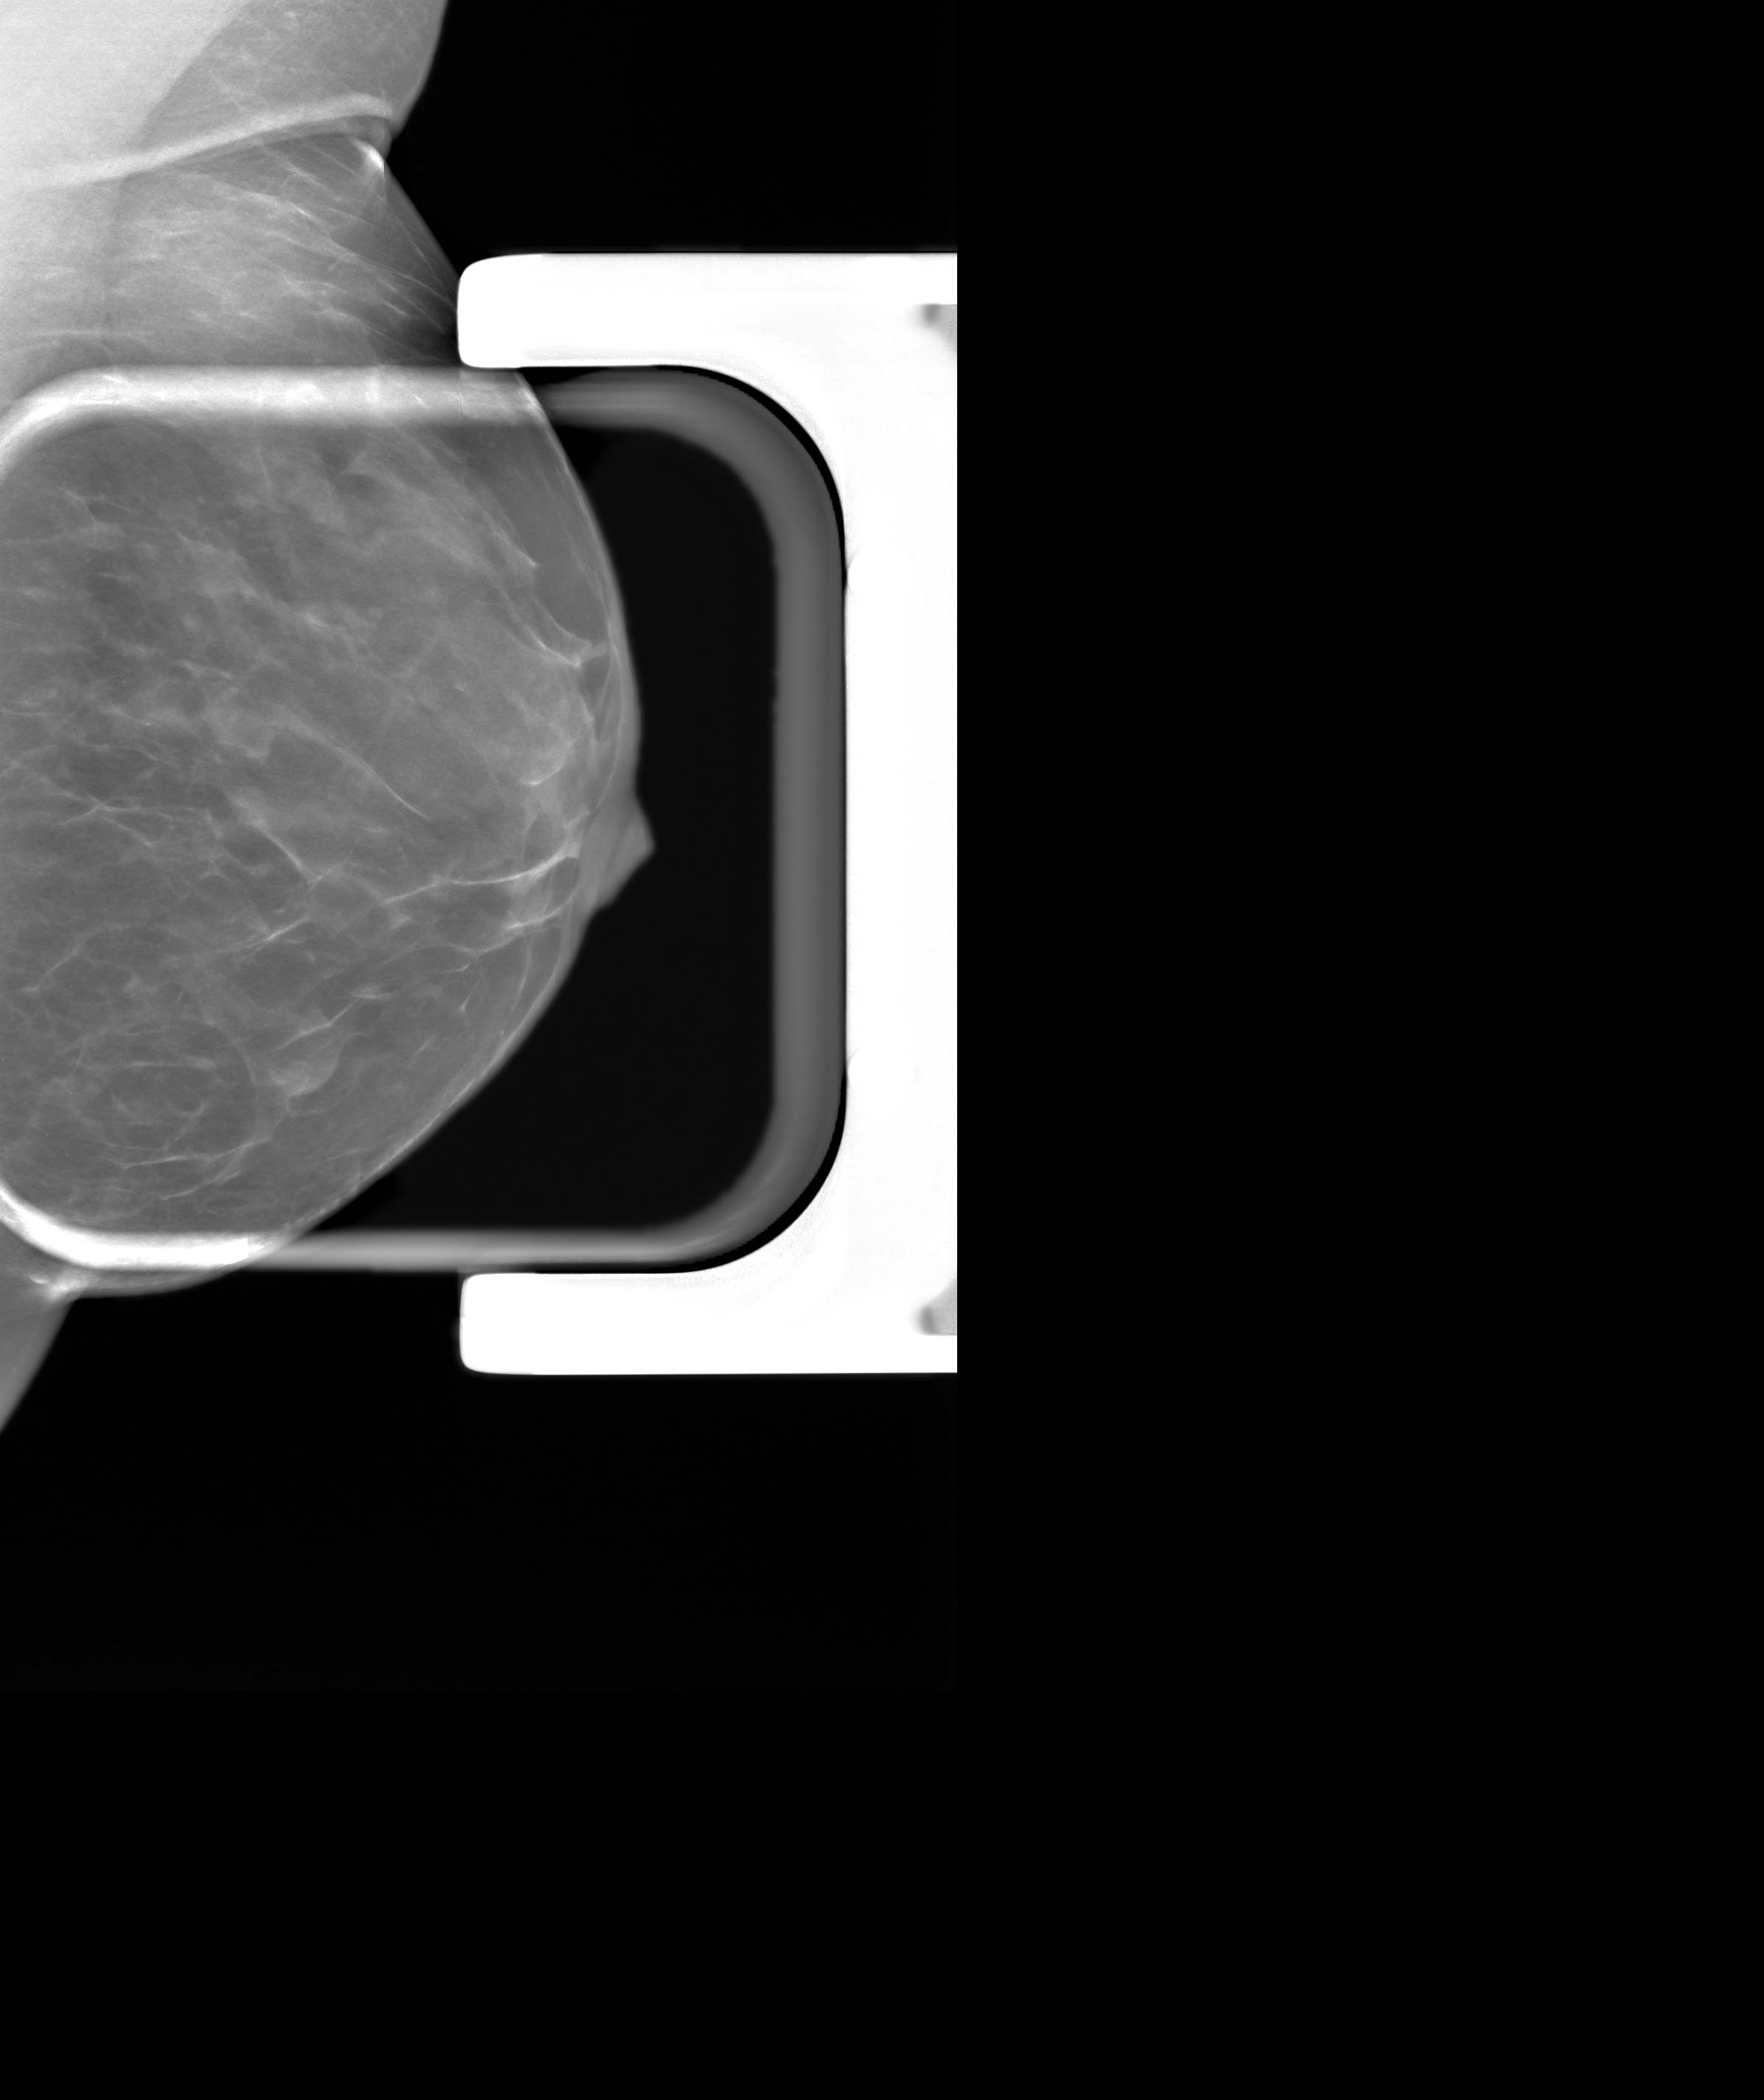
Additional (diagnostic) view, system: SenoIris_1SP1.2(425). Patient aged 49 years (female).
Image type: synthesized 2-D view from tomosynthesis. Breast: left. Projection: mediolateral oblique (MLO) view, spot compression.